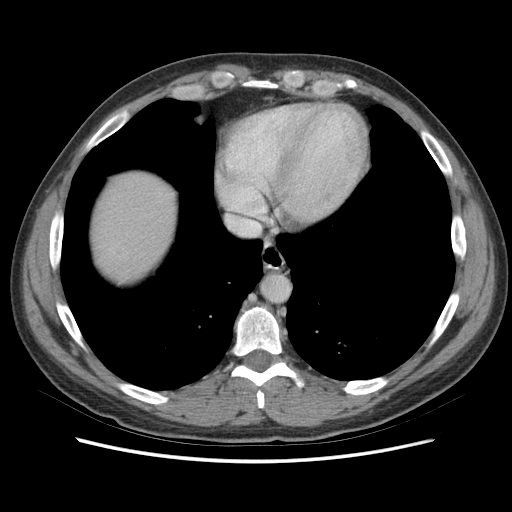
Contrast-enhanced abdominal CT (liver protocol), one axial slice. Position 68 of 73 along the scan axis. 140 kVp. Soft-tissue window (W 400 / L 40 HU). 2.5 mm slice thickness. 512 × 512 image matrix, field of view 360 × 360 mm. Case-level facts recorded for this patient, not image findings: diagnosis: hepatocellular carcinoma (patient treated with transarterial chemoembolisation; whether this scan precedes or follows treatment is not stated here); TNM stage (as recorded): Stage-IIIA; Child-Pugh class: A.
Annotated regions visible in this slice (semi-automatically segmented with operator editing):
- abdominal aorta: bounding box (x1, y1, x2, y2) in pixels: (263, 276, 290, 301)
- liver parenchyma outside the tumour (the mass and vessels are separate outlines, so this box may not span the whole liver): (92, 172, 174, 280)